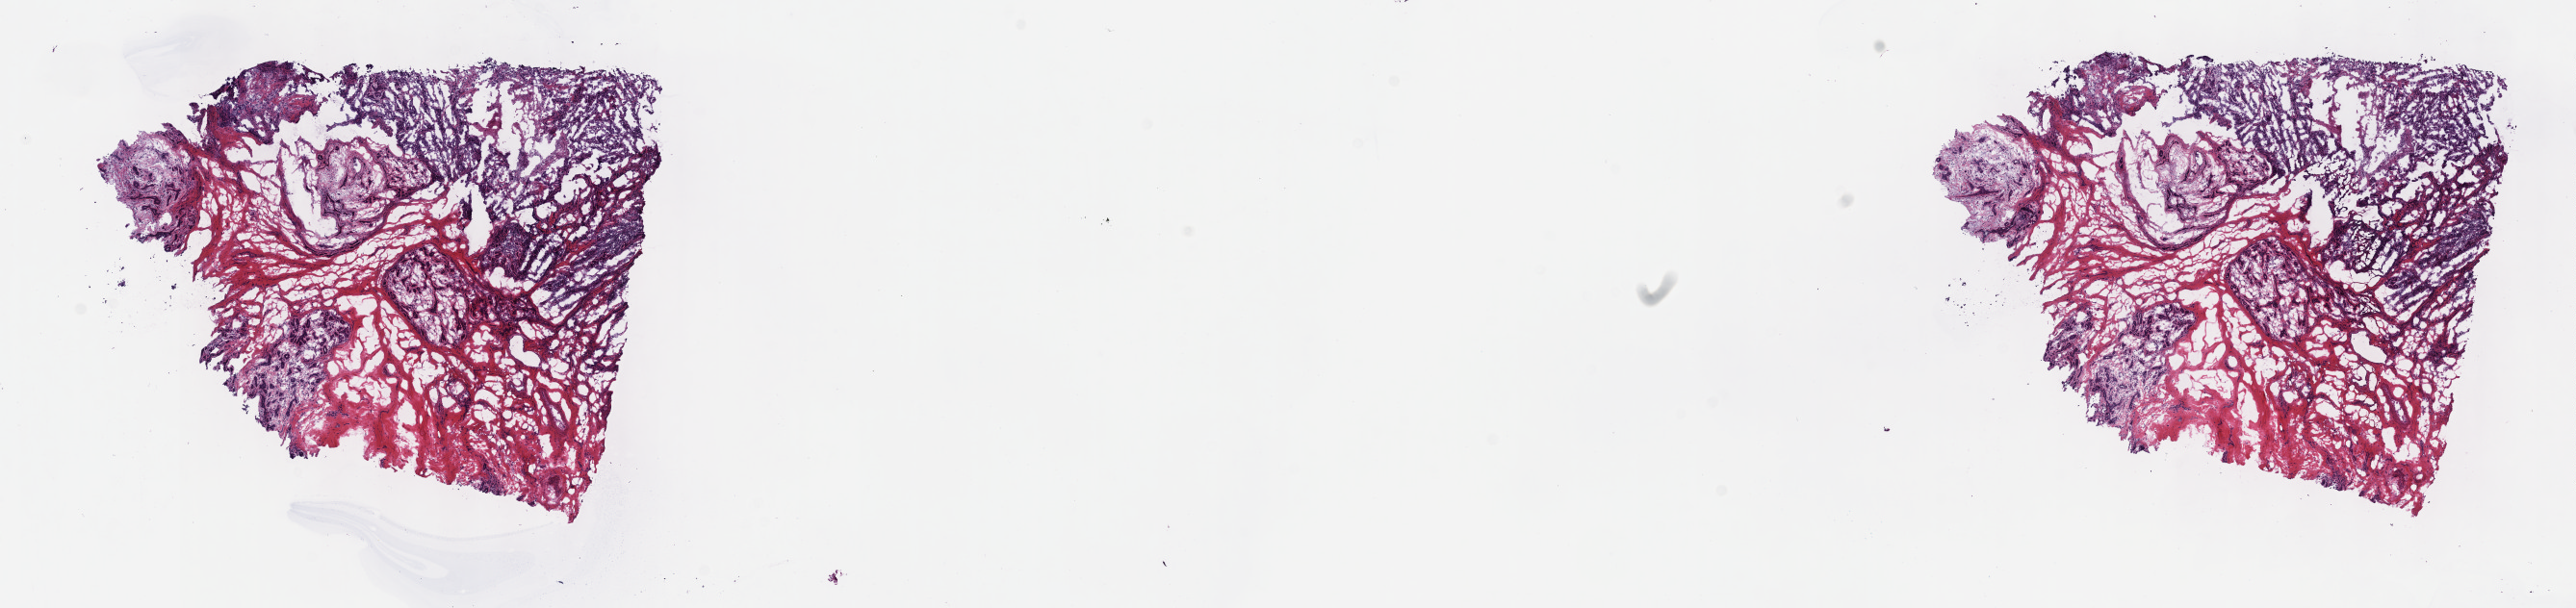
Digitized H&E-stained tissue section (whole slide) — whole scanned area (about 21.6 x 5.1 mm, slide scanned at 40x) shown as a low-resolution overview. Formalin-fixed paraffin-embedded (FFPE) diagnostic section. Sample: primary tumour, breast. Patient: female, age at initial diagnosis 30 years.
Pathologic diagnosis: Infiltrating duct carcinoma, NOS.